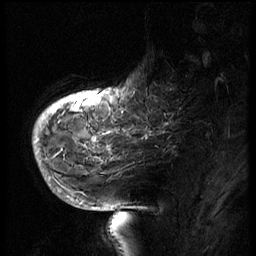
Breast MRI (dynamic contrast-enhanced), one sagittal slice; position 14 of 66 along the scan axis; 3 images stored at this slice position (order not interpretable as contrast timing); 1.5 T; TE 4.2 ms, TR 8.9 ms; 2.5 mm slice thickness; 256 × 256 image matrix. Patient: female, 56 years. From the clinical record (not read from this slice): setting: breast cancer imaged before/during neoadjuvant chemotherapy.
Structures marked on this image (semi-automatically segmented with operator editing):
- analysis volume of interest (the breast-tissue region the enhancement analysis was run in; not a lesion): bounding box <129,62,194,127> (left, top, right, bottom; pixels)
- tumour enhancement mask (voxels above the 140 % enhancement threshold inside the analysis volume of interest): <129,90,173,126>